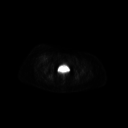
FDG PET of an extremity soft-tissue mass (from a PET/CT study), one axial slice. Slice 67 of 267 in the series (ordered by position). 3.27 mm slice thickness. 128 × 128 image matrix, field of view 700 × 700 mm. Female patient, age 56 years. From the clinical record (not read from this slice): histological type: malignant solitary fibrous tumor; grade: intermediate; site of the primary tumour: right thigh.
Structures marked on this image (expert contour drawn on MRI and transferred to this co-registered scan by the dataset authors):
- gross tumour volume including surrounding oedema: bounding box [x1, y1, x2, y2] px = [37, 55, 48, 62]